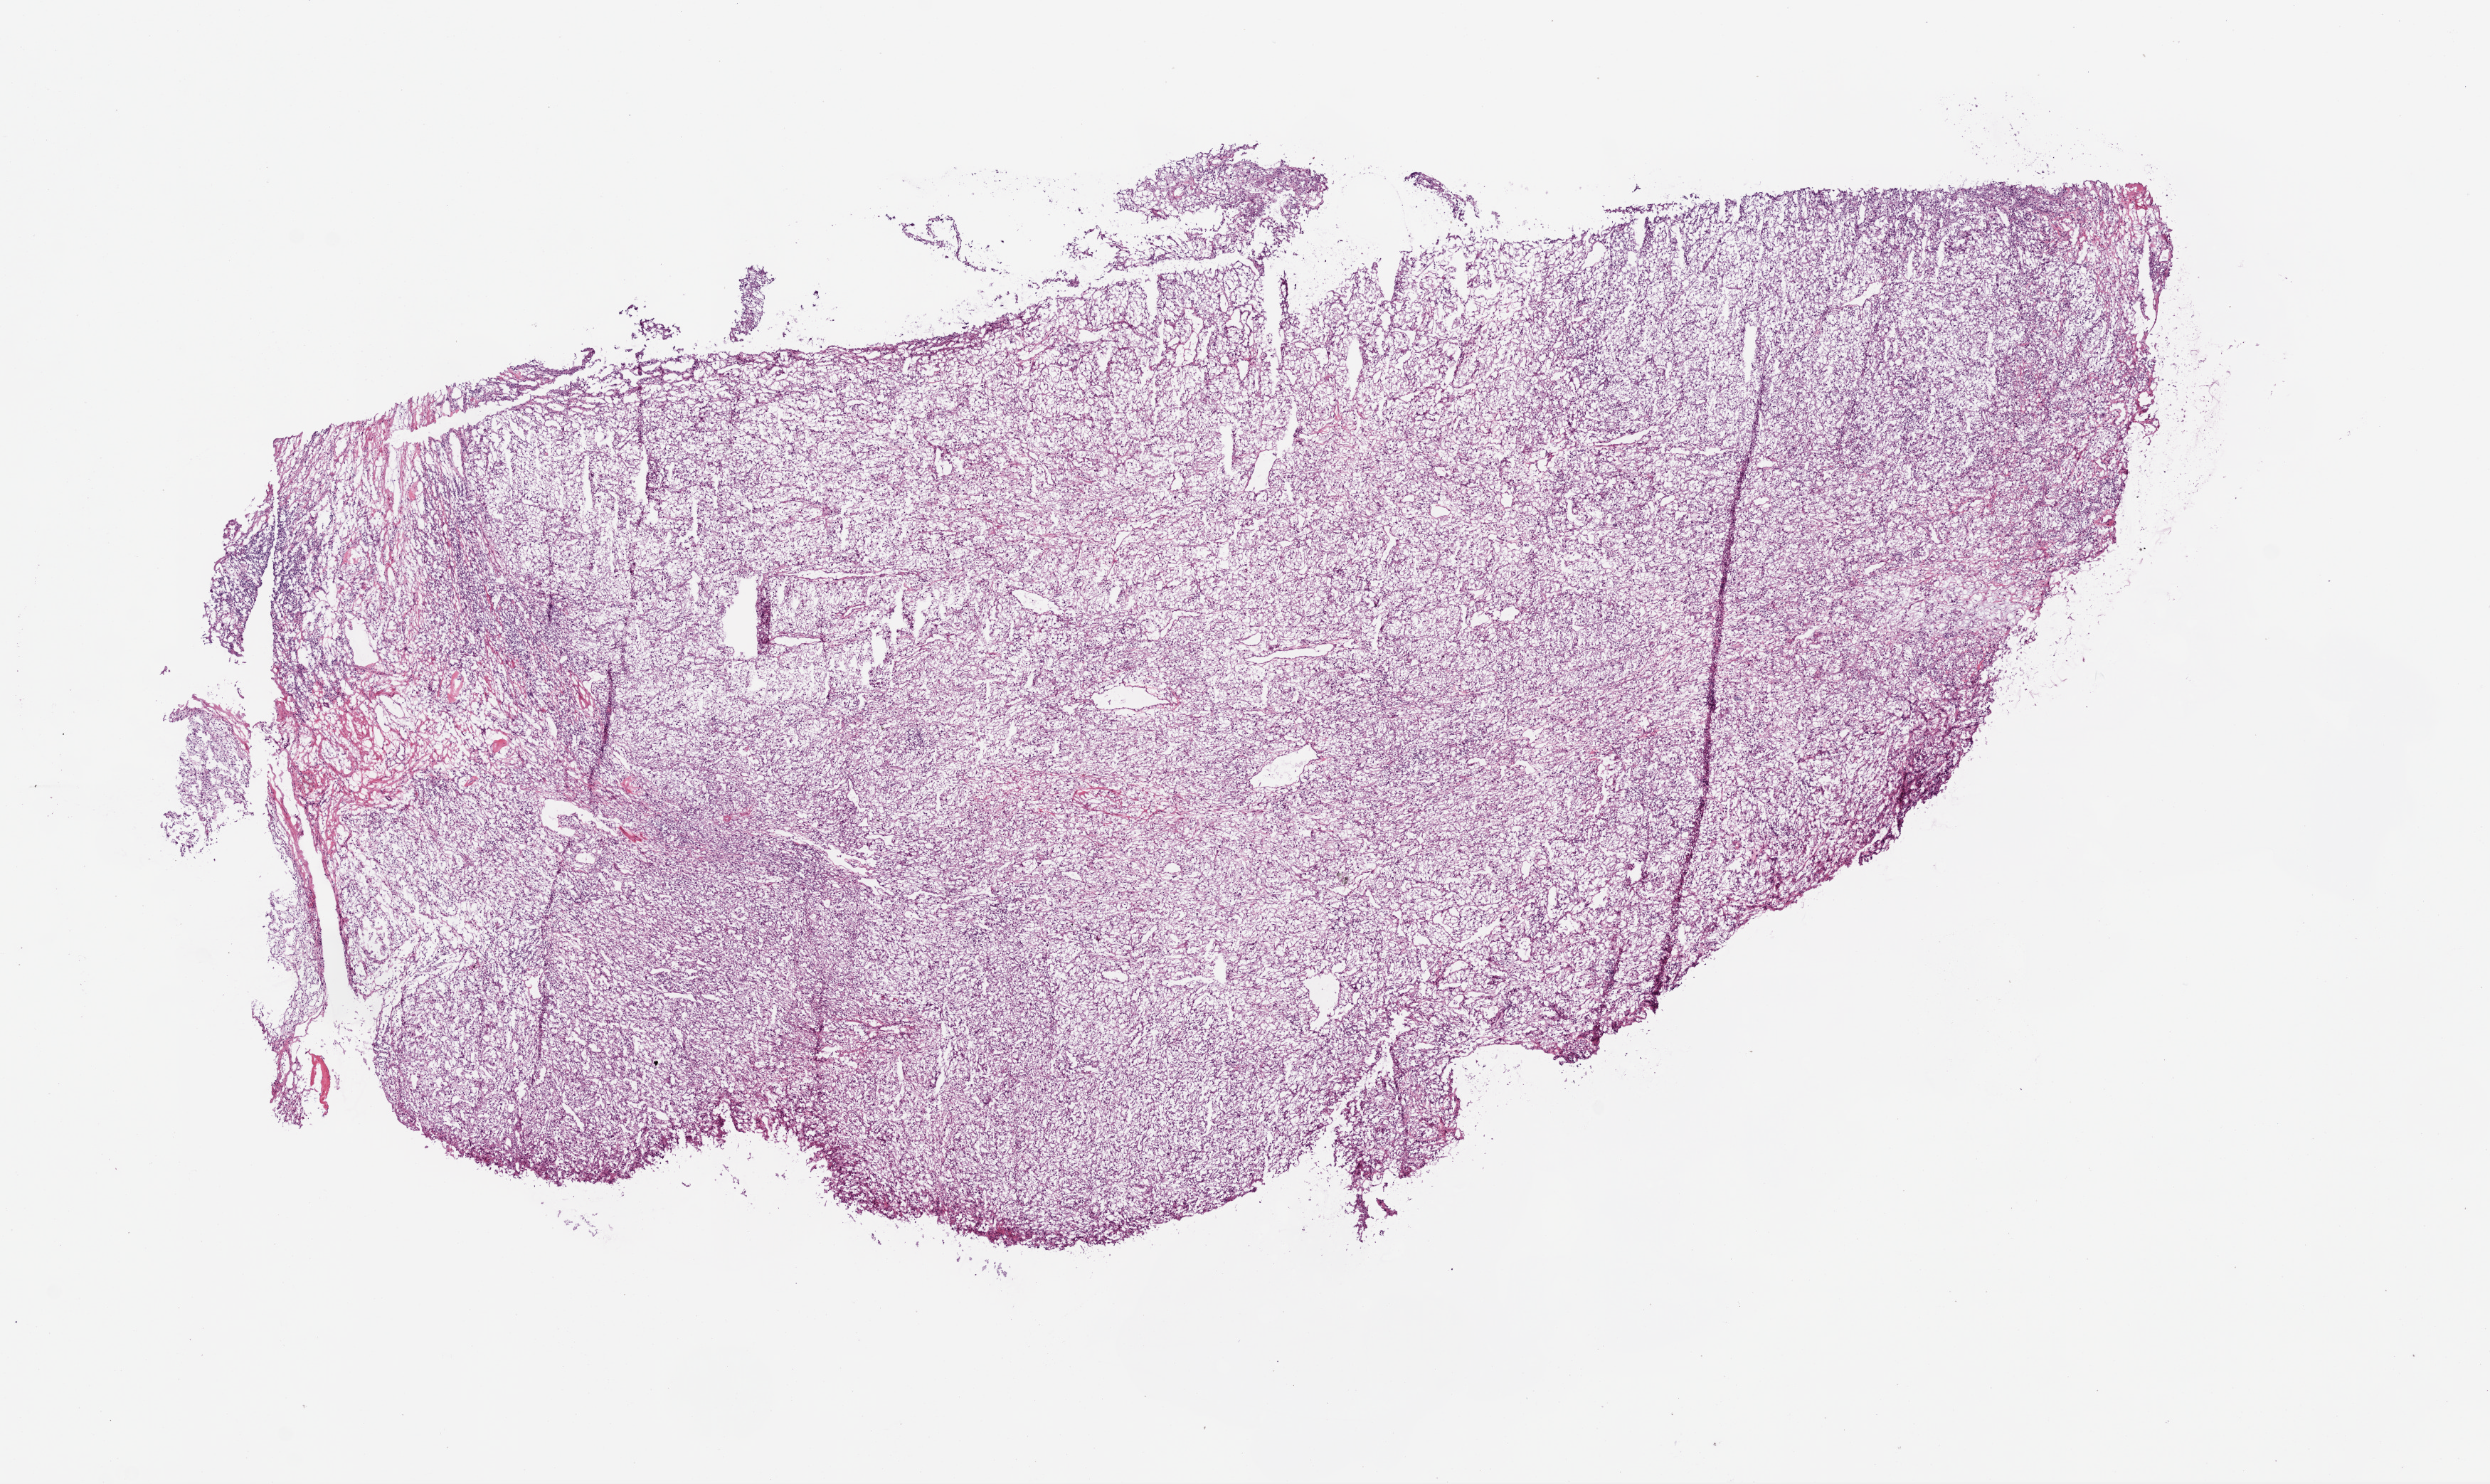
H&E whole-slide image, low-resolution overview of the scanned area, about 14.0 x 8.4 mm (acquisition: 20x scan); frozen section from the top of the tissue portion; kidney, primary tumour sample. Patient: female, age at initial diagnosis 79 years. Histologic grade: G2 (moderately differentiated). Slide review estimates, as recorded: tumour cells 90%, tumour nuclei 80%, normal cells 0%, stromal cells 10%, necrosis 0%.
AJCC pathologic stage: III. Histologic diagnosis: Clear cell adenocarcinoma, NOS.